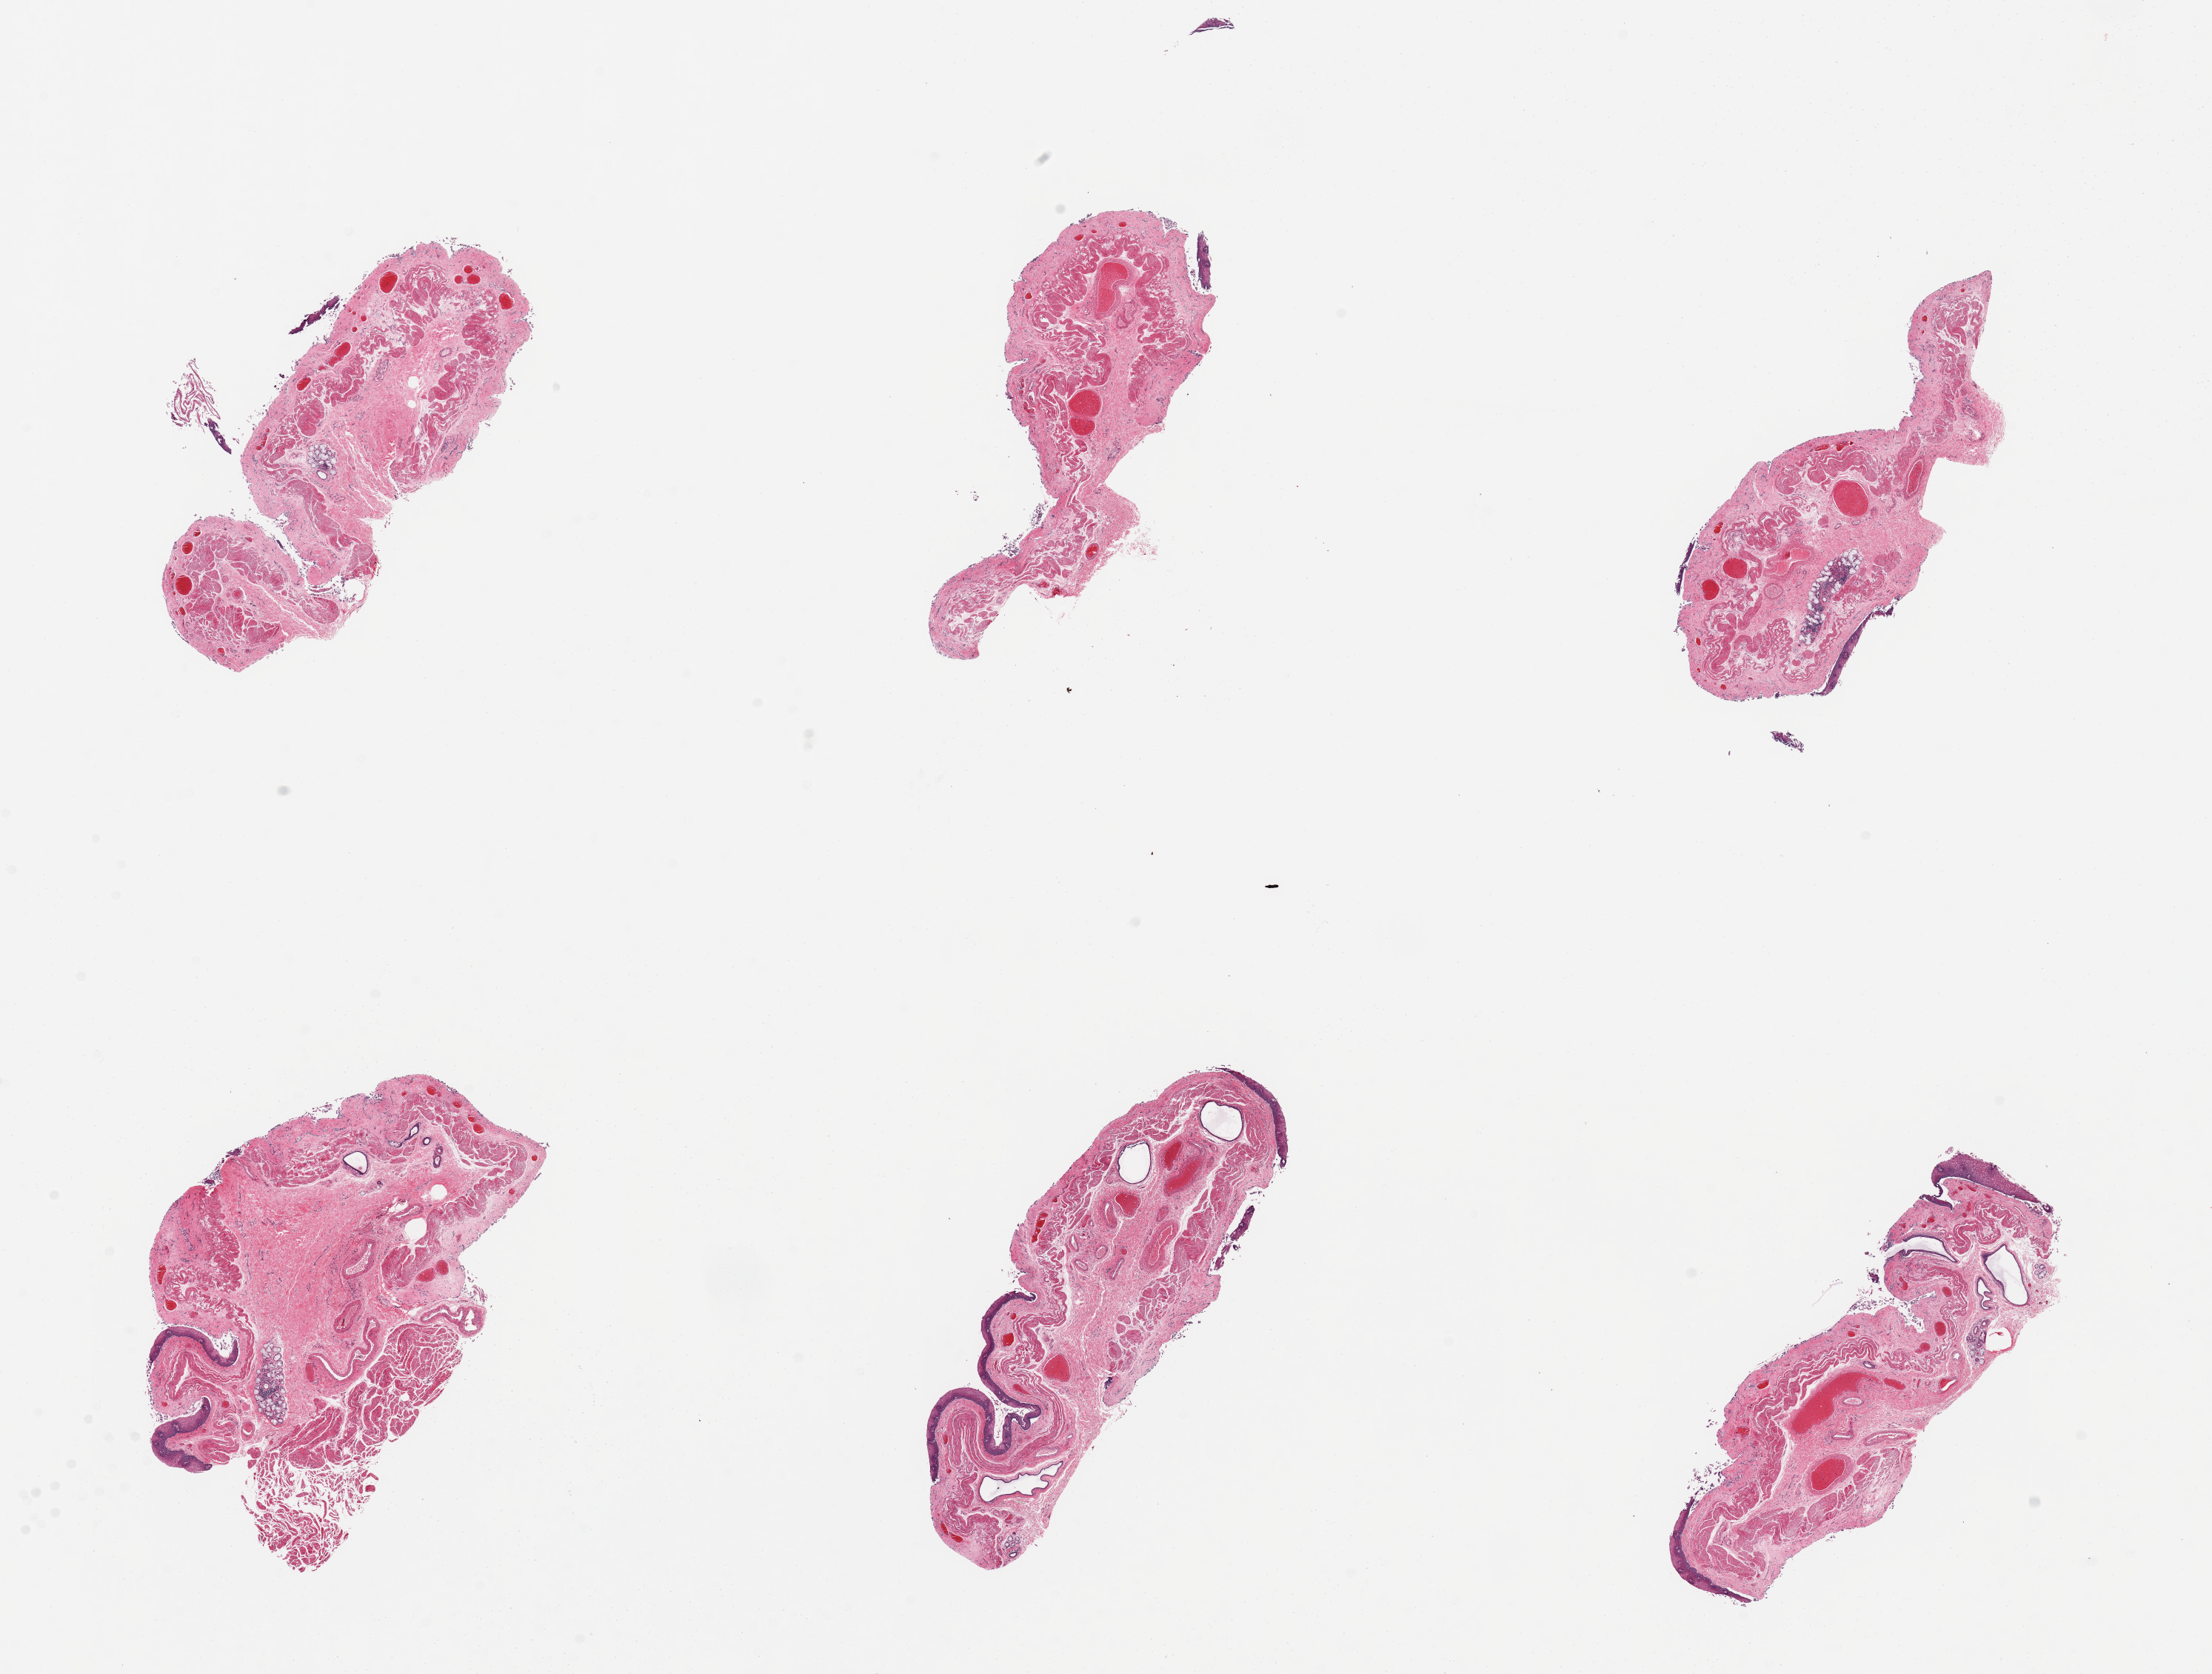
Haematoxylin and eosin whole-slide image — low-resolution overview of the scanned area, about 23.6 x 17.9 mm (acquisition: 20x scan); PAXgene-fixed, paraffin-embedded tissue; target tissue: esophageal mucous membrane; tissue donor sample. Male donor.
Pathologist's review note for this sample: 6 pieces; only isolated pieces of squamous epithelium remain unsloughed.